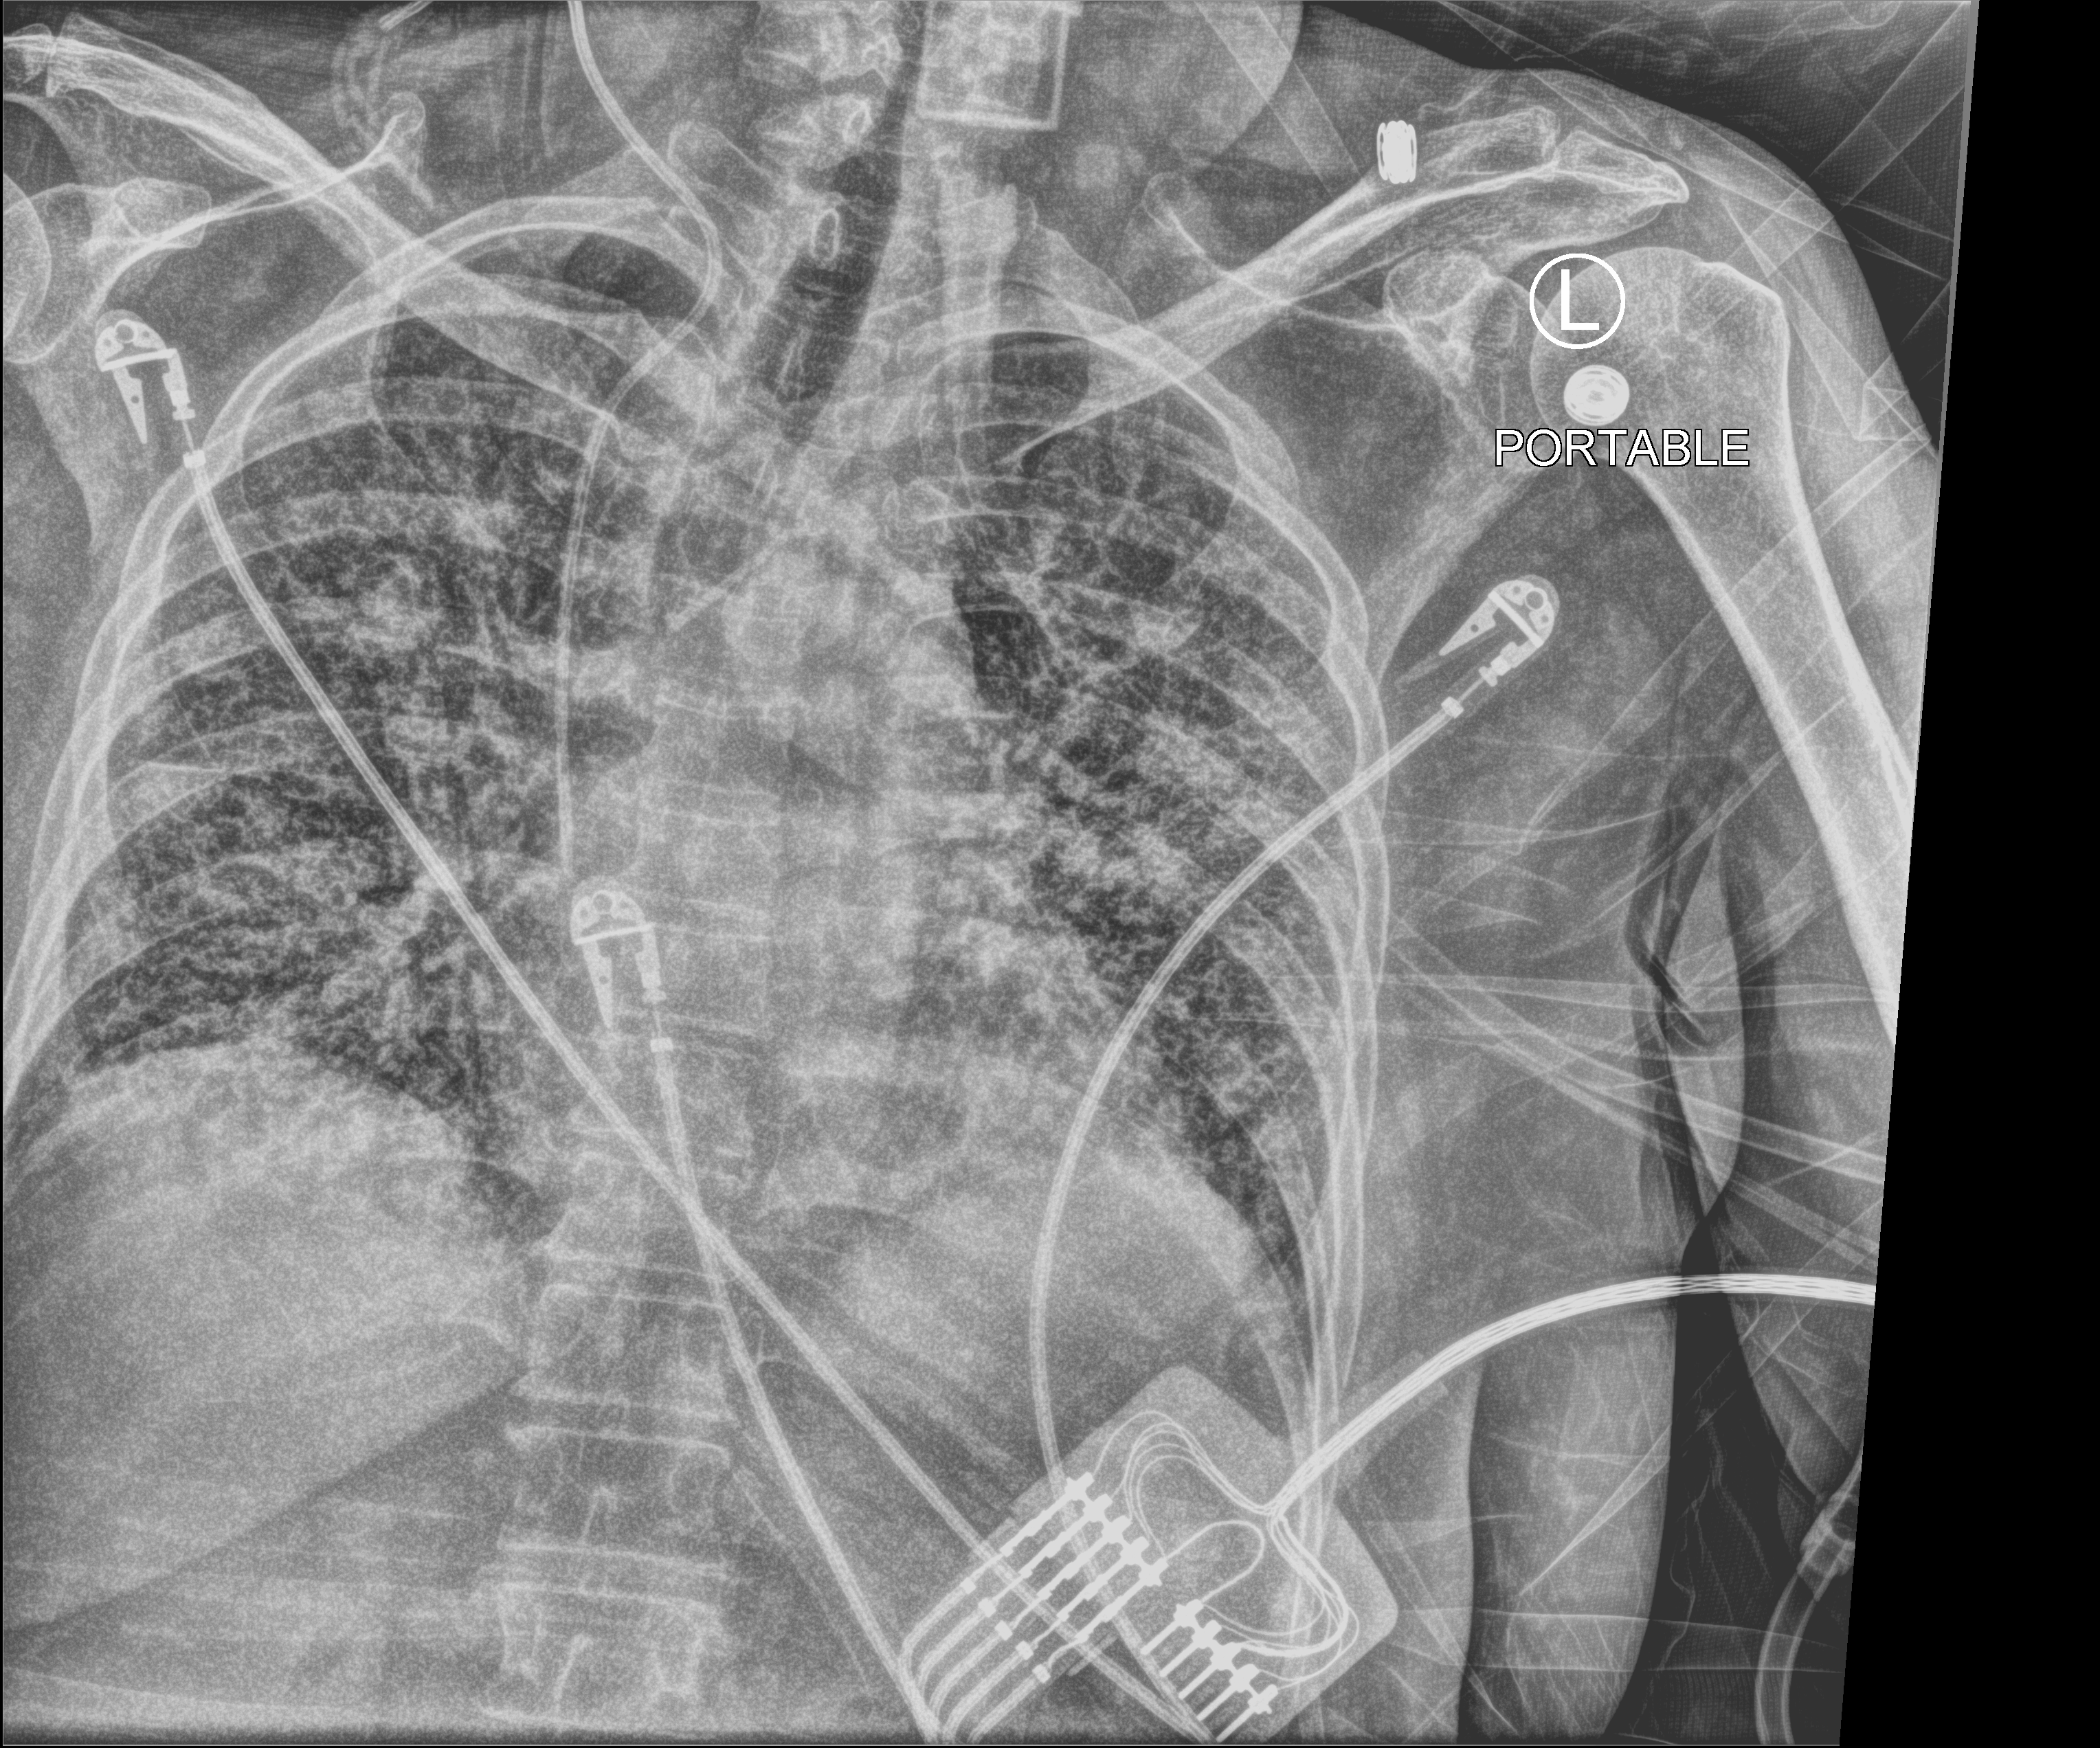
Chest X-ray (portable); anteroposterior (AP) projection. Patient hospitalised with COVID-19; female, aged 60–74 years.
Hospital-stay facts (about this admission, not read from this image; timing relative to this image not recorded): COPD (admission record): no.